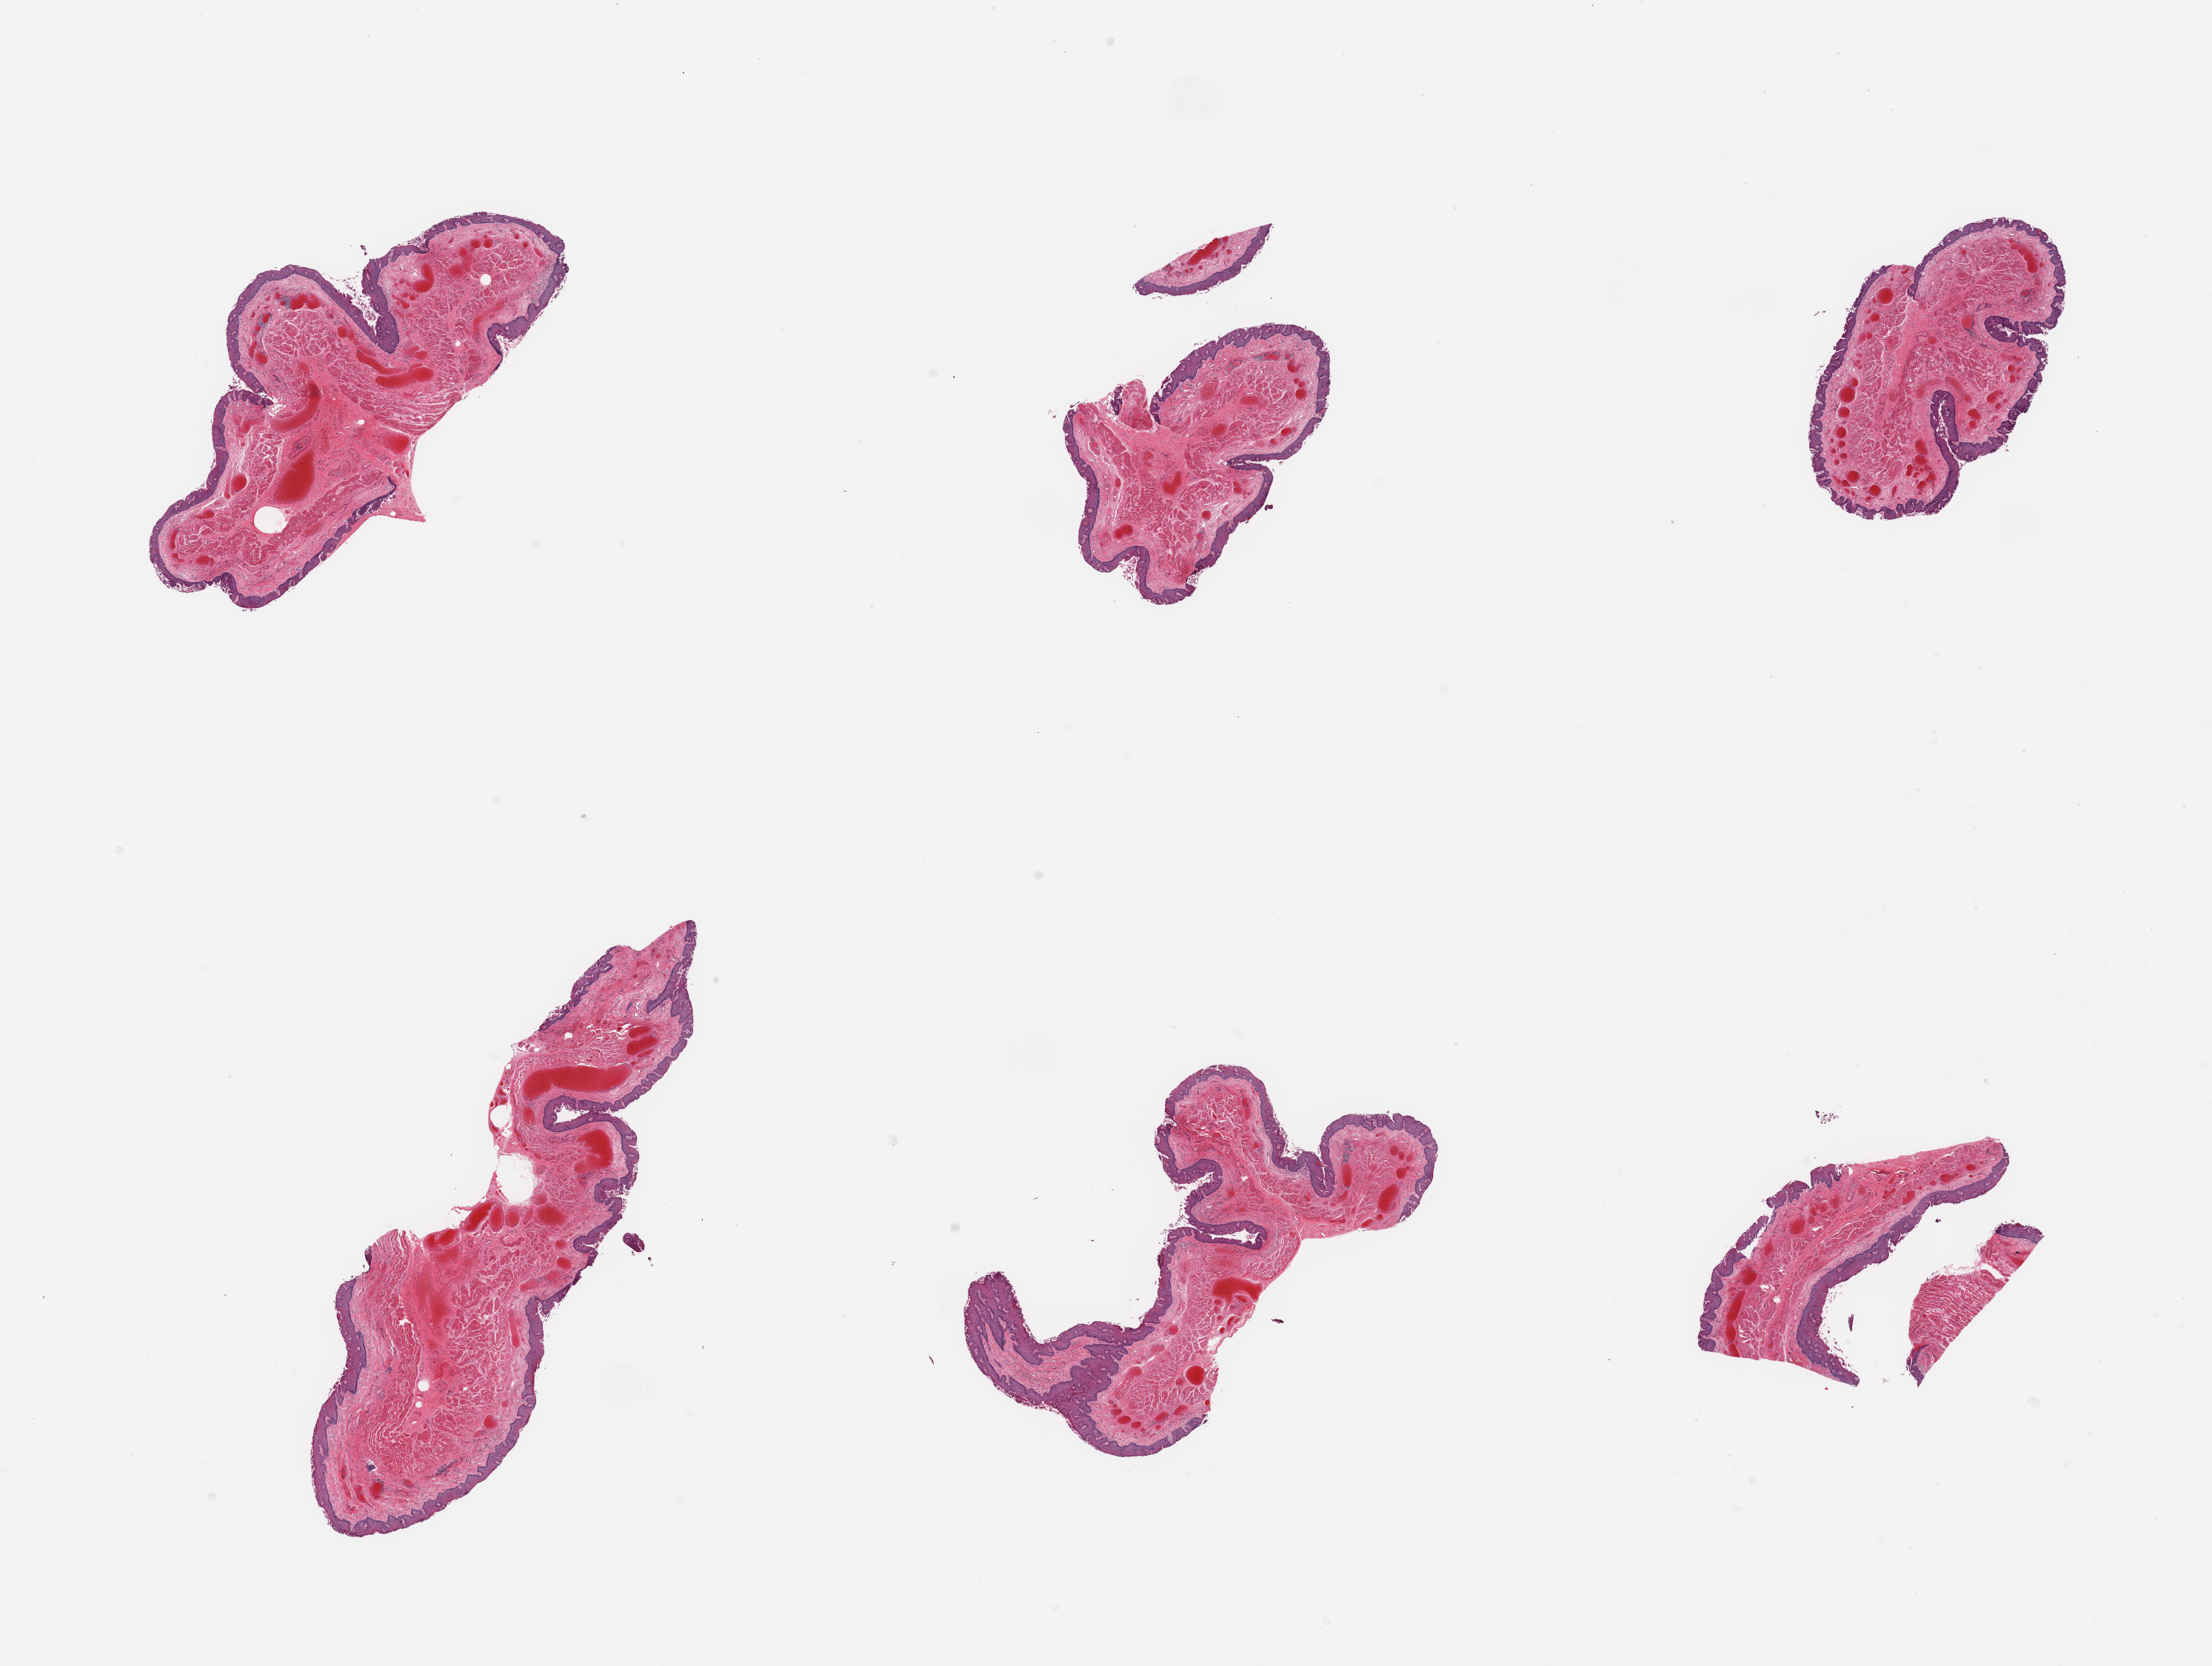
Whole-slide image, haematoxylin and eosin stain, low-resolution overview of the scanned area, about 23.6 x 17.8 mm; PAXgene-fixed paraffin-embedded (PFPE) section; target tissue: esophageal mucous membrane; donor tissue sample. Donor: male.
Reviewer comment on this tissue sample: 6 pieces; moderate epithelial fragmentation; well dissected.